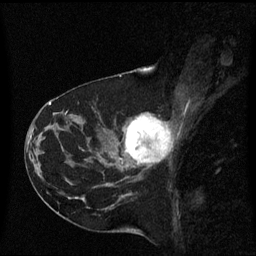
Breast MRI (dynamic contrast-enhanced), one sagittal slice. Slice 29 of 60 in the series (ordered by position). Dynamic contrast-enhanced series, image 2 of 3 at this slice position (ordered by acquisition). 1.5 T. TE 4.2 ms, TR 8.4 ms. 256 × 256 image matrix. Patient: female, 41 years. From the clinical record (not read from this slice): setting: breast cancer imaged before/during neoadjuvant chemotherapy; receptor status: triple-negative.
Outlined on this slice (semi-automatic segmentation, software-assisted and operator-edited):
- analysis volume of interest (the breast-tissue region the enhancement analysis was run in; not a lesion): bounding box [x1, y1, x2, y2] px = [116, 114, 173, 177]
- tumour enhancement mask (voxels above the 70 % enhancement threshold inside the analysis volume of interest): [125, 114, 171, 165]